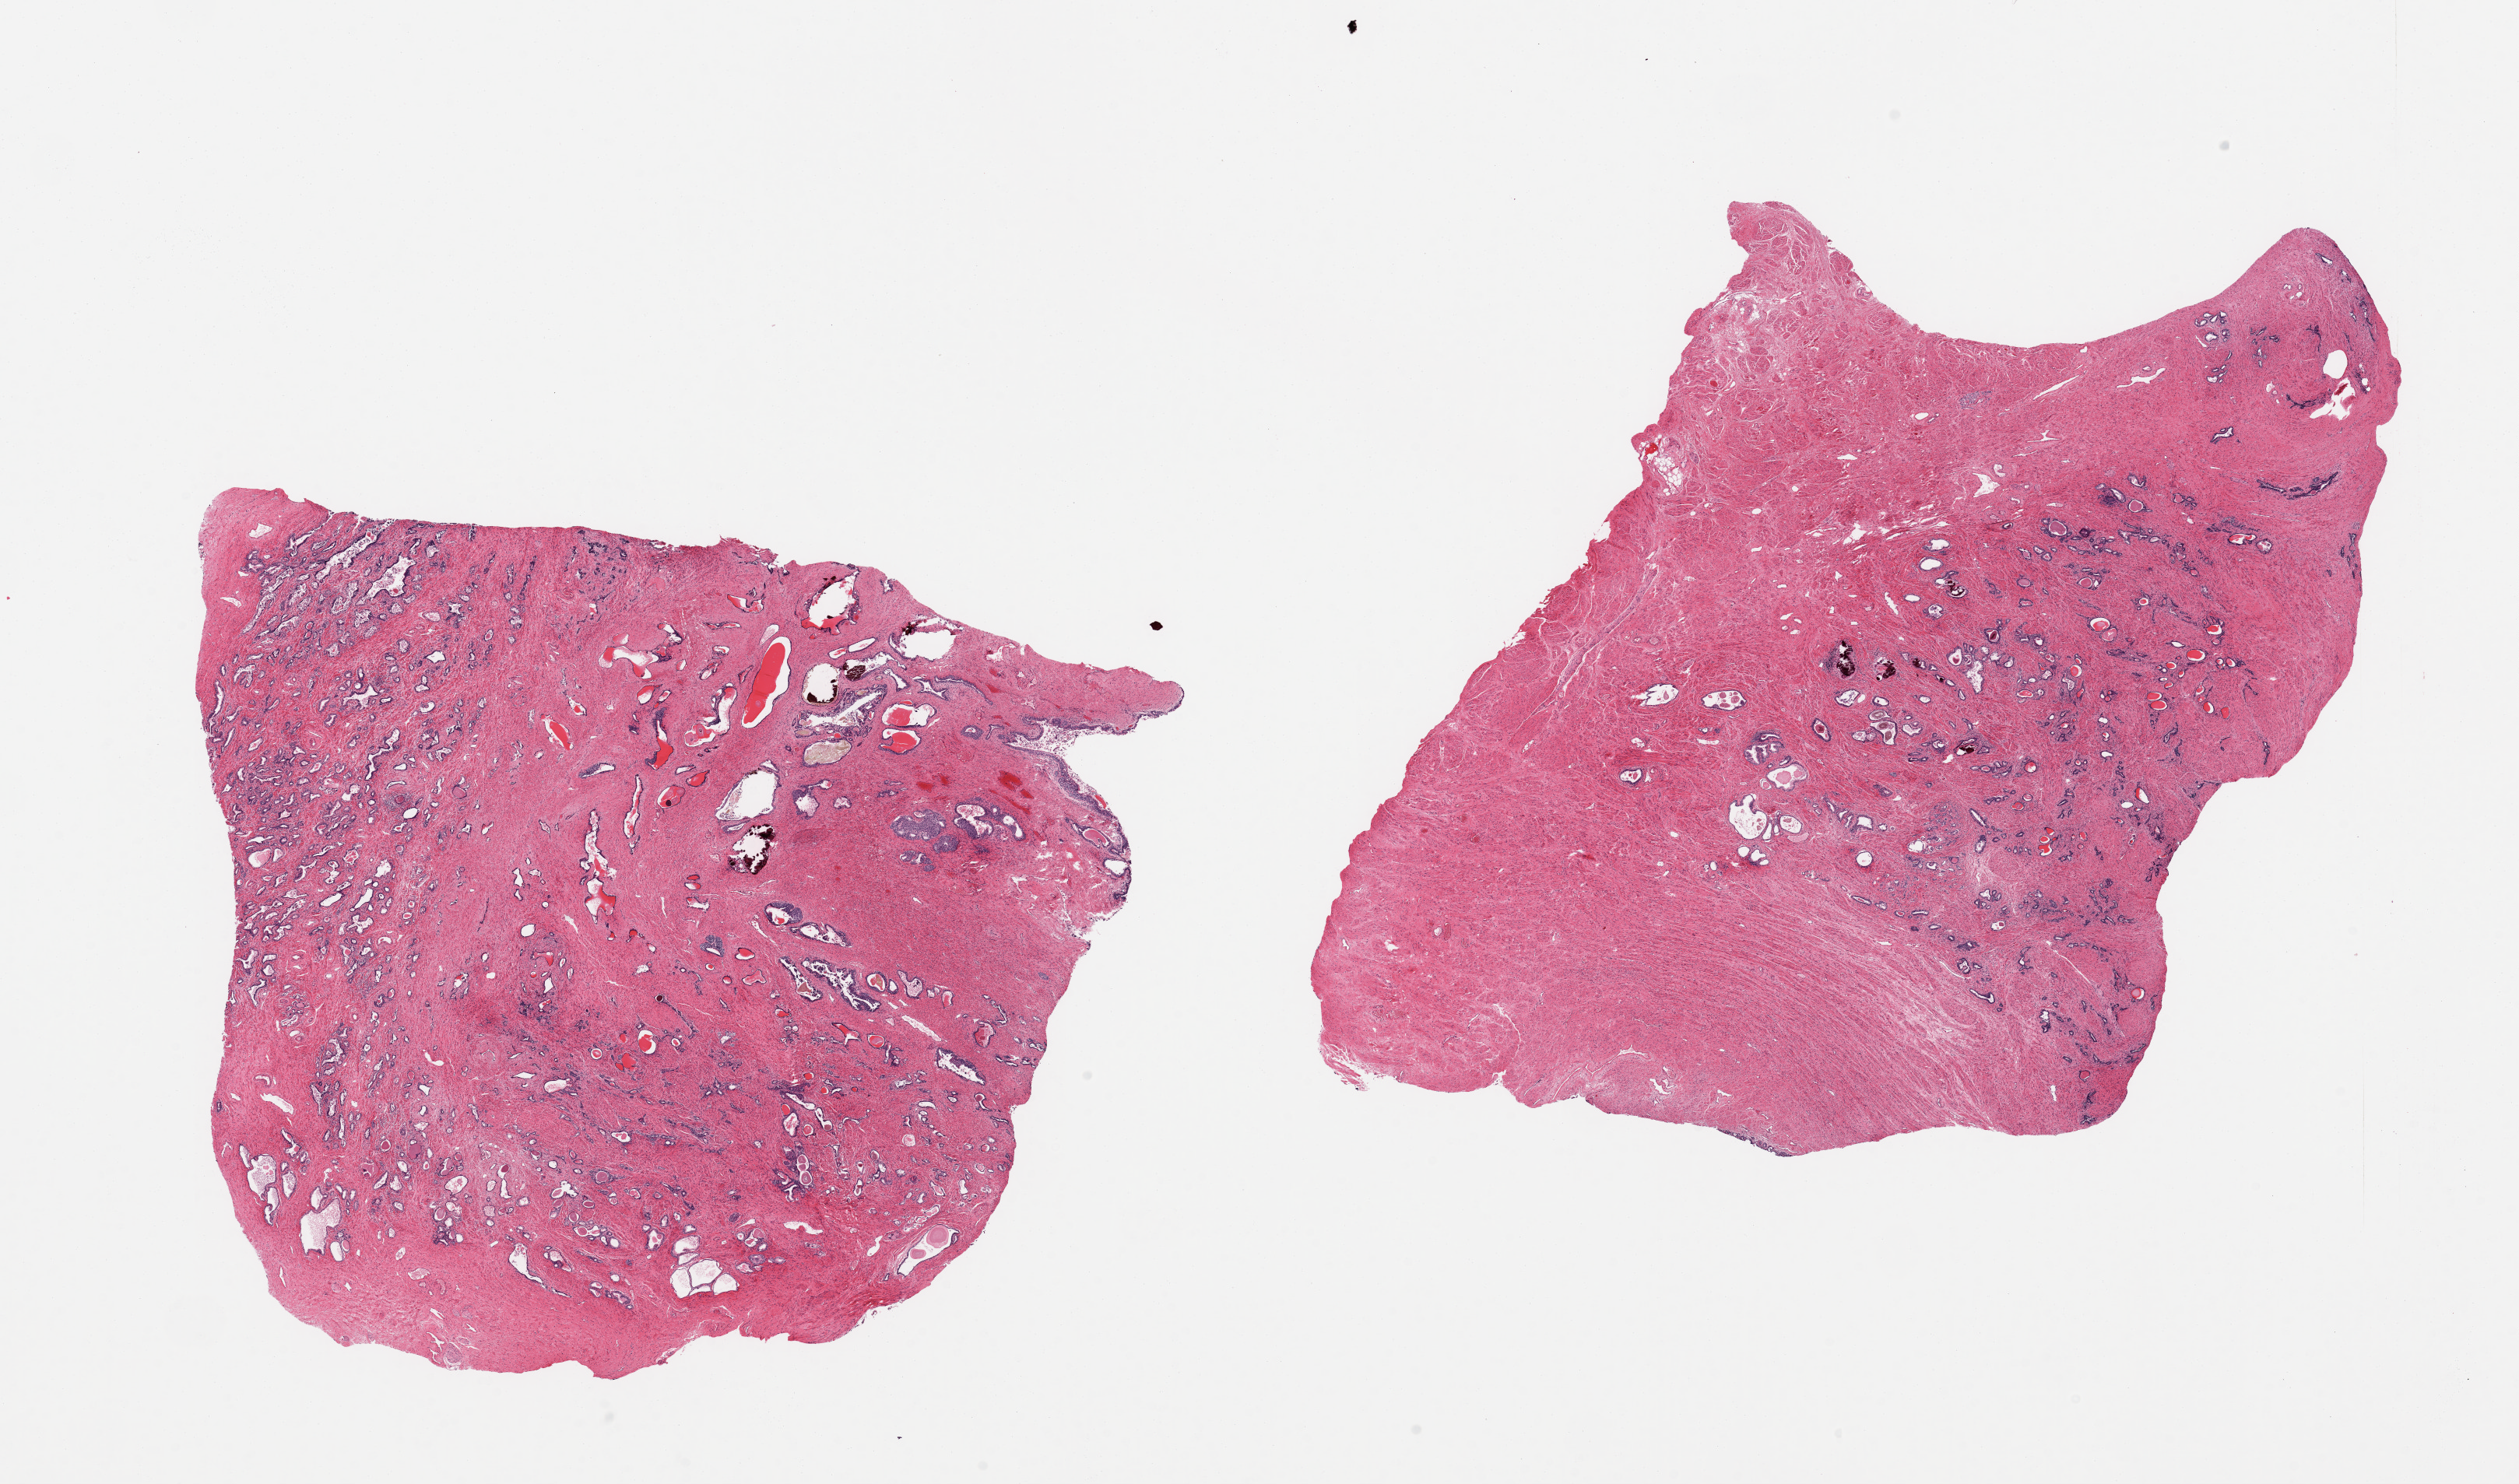
Hematoxylin and eosin (H&E) whole-slide image — low-resolution overview of the scanned area, about 25.6 x 15.1 mm (acquisition: 20x scan); PAXgene-fixed paraffin-embedded (PFPE) section; section of prostate (target tissue); donor tissue sample. Donor: male.
• review note (as recorded): 2 pieces; no nodular hyperplasia